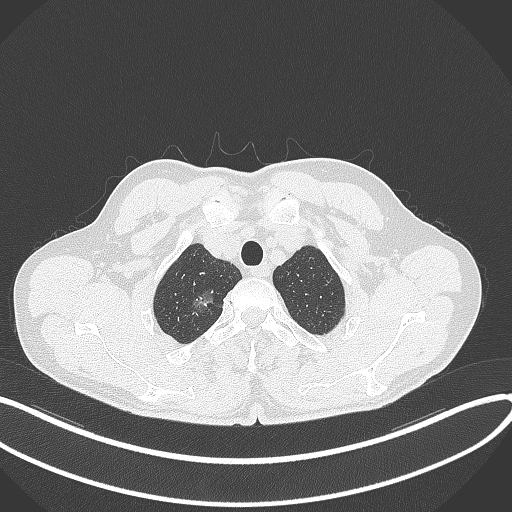
Chest CT, one axial slice. Slice 342 of 407 in the series (ordered by position). 120 kVp. Lung window (W 1500 / L -600 HU). 512 × 512 image matrix, field of view 400 × 400 mm. Patient: male, 58 years. Case-level facts recorded for this patient, not image findings: clinical TNM (as recorded): T1c N0 M0.
Outlined on this slice (rectangle marked by the reading radiologist):
- lung tumour (recorded histology: adenocarcinoma): bounding box <188,289,225,317> (left, top, right, bottom; pixels)